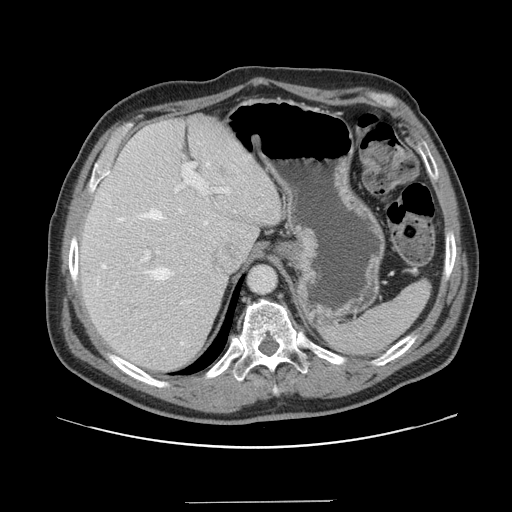
Contrast-enhanced abdominal CT, one axial slice. Position 113 of 151 along the scan axis. 120 kVp. Intravenous contrast given. Soft-tissue window (W 400 / L 40 HU). 2.5 mm slice thickness. 512 × 512 image matrix, field of view 399 × 399 mm. Male patient, age 63 years. Case-level facts recorded for this patient, not image findings: diagnosis: colorectal cancer liver metastases, imaged before liver resection; multiple liver metastases: no; largest metastasis: 2.1 cm; disease in both lobes: no.
Structures marked on this image (expert manual segmentation):
- hepatic veins: box from (x=102, y=162) to (x=210, y=280) px
- liver: (x=78, y=116)–(x=281, y=373)
- planned liver remnant (the part of the liver to remain after resection): (x=79, y=118)–(x=266, y=372)
- portal vein (with intrahepatic branches): (x=141, y=163)–(x=230, y=304)
- liver metastasis: (x=218, y=169)–(x=227, y=176)